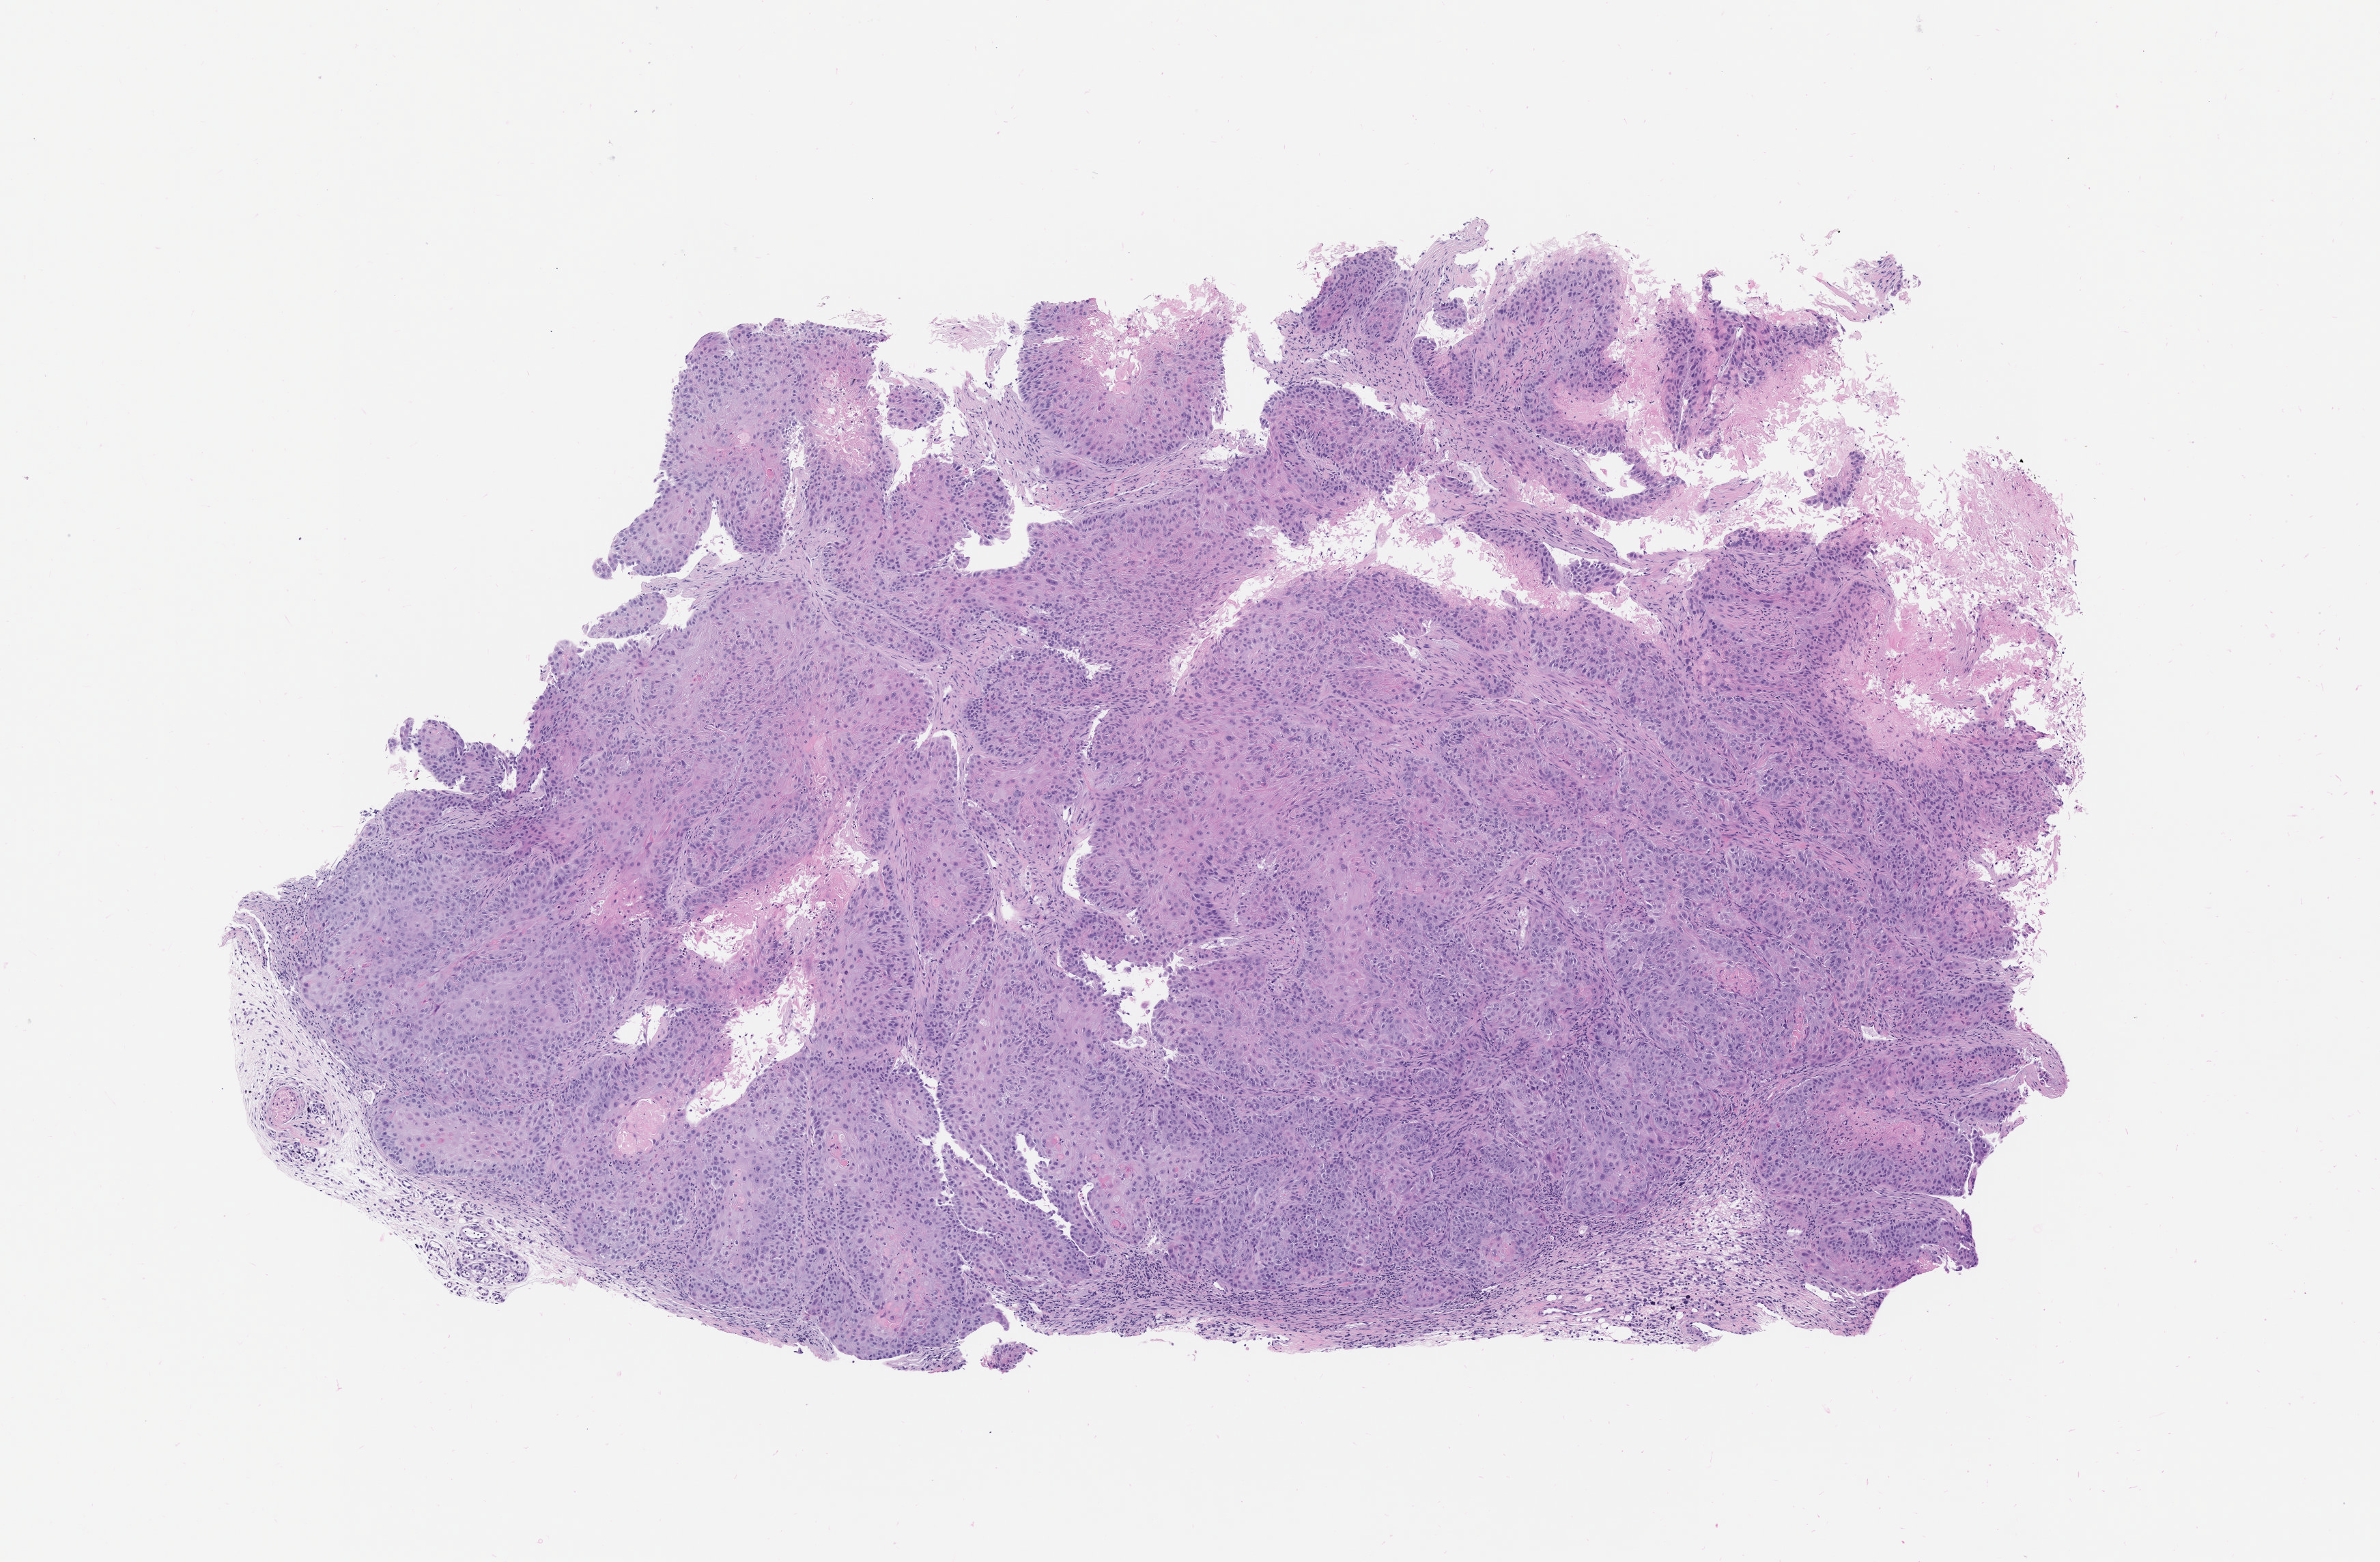
Whole-slide image, hematoxylin and eosin (H&E): patient-derived xenograft (human tumor grown in a mouse), passage 2, a low-resolution overview of the entire scanned area, about 7.0 x 4.6 mm. FFPE section. Originating tumor site category: lung.
Originating patient diagnosis: Lung Squamous Cell Carcinoma.